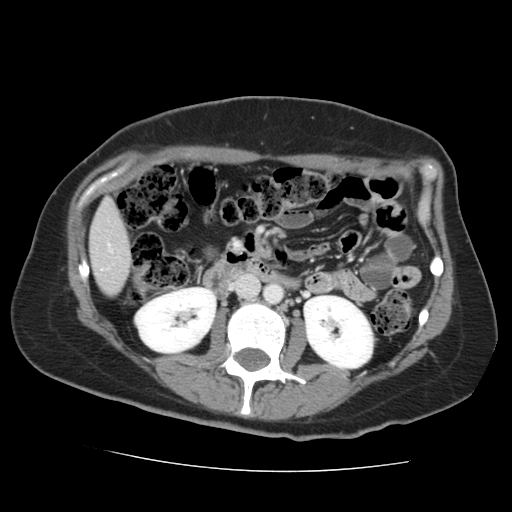
Contrast-enhanced abdominal CT, one axial slice. Position 50 of 144 along the scan axis. Intravenous contrast given. Soft-tissue window (W 400 / L 40 HU). 512 × 512 image matrix, field of view 333 × 333 mm. Female patient, age 46 years. Case-level facts recorded for this patient, not image findings: diagnosis: colorectal cancer liver metastases, imaged before liver resection; multiple liver metastases: no; largest metastasis: 2.8 cm; disease in both lobes: no.
Structures marked on this image (expert manual segmentation):
- liver: bounding box <91,202,130,295> (left, top, right, bottom; pixels)
- planned liver remnant (the part of the liver to remain after resection): <91,202,130,295>